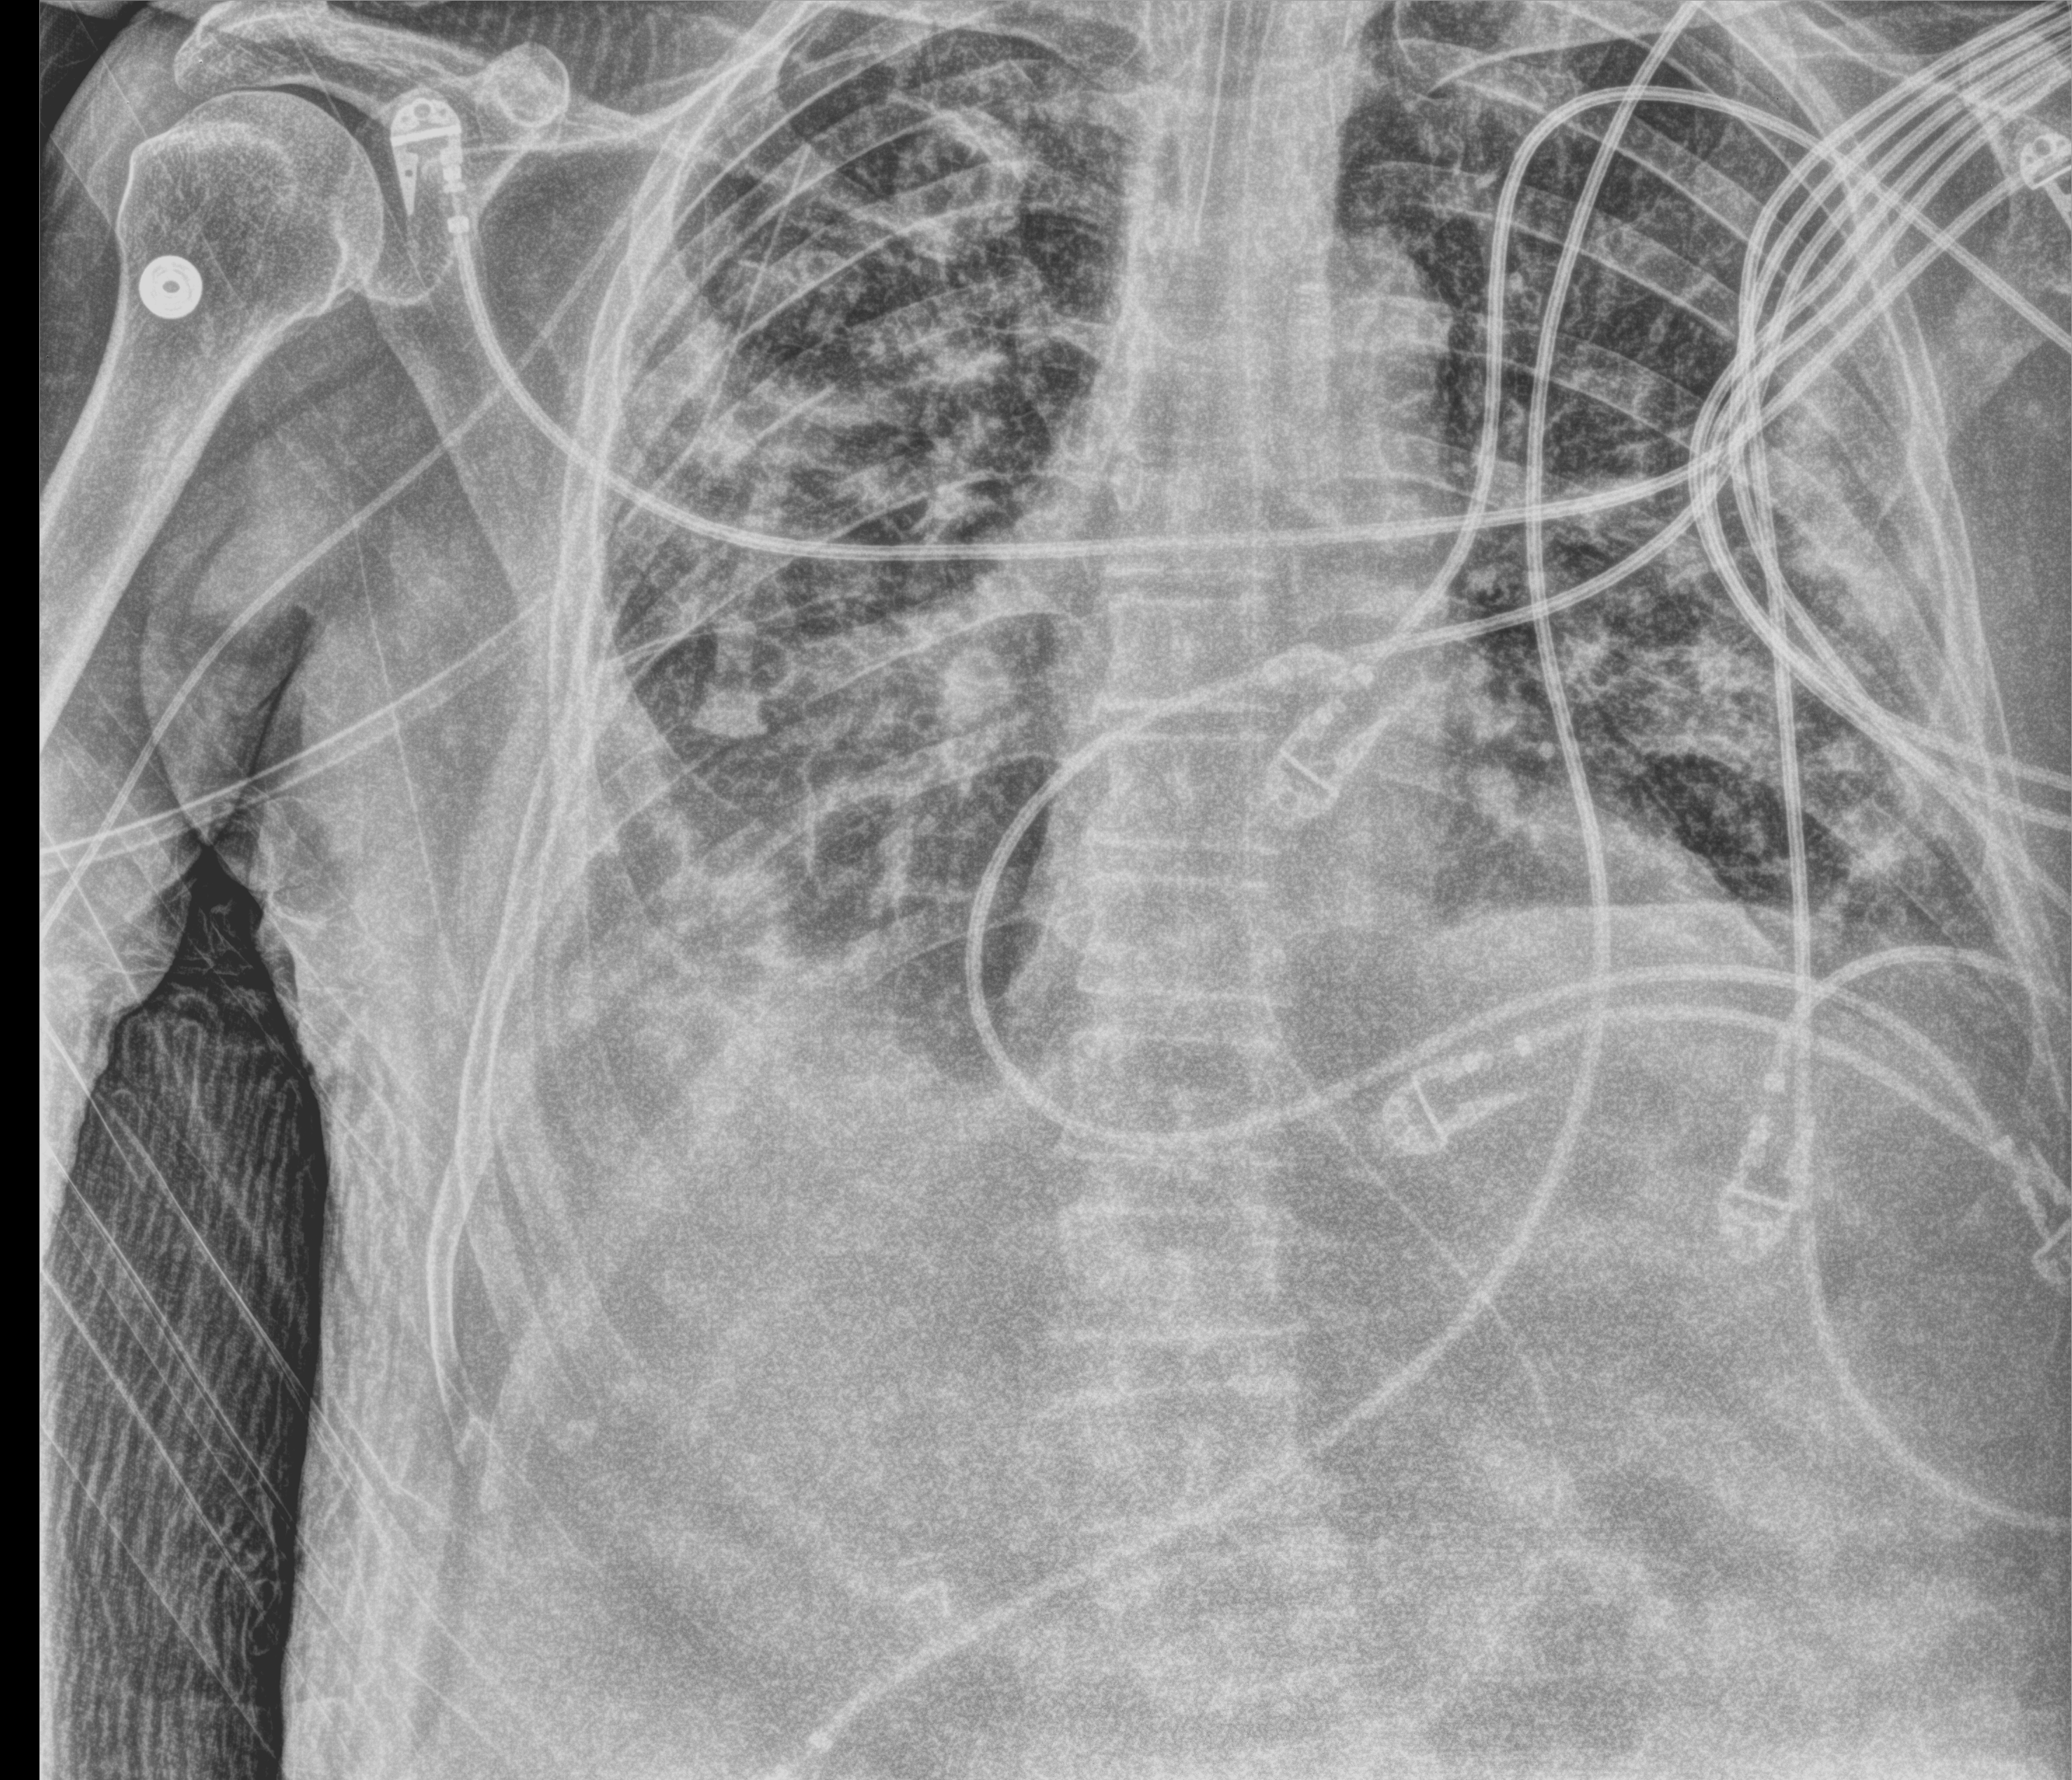
Bedside chest radiograph (computed radiography); anteroposterior (AP) projection. Patient hospitalised with COVID-19; male, aged 75–90 years.
From the hospital-stay record, not from the radiograph (when in the stay this image was taken is not recorded): mechanically ventilated during this hospital stay: yes; admitted to intensive care during this hospital stay: yes.